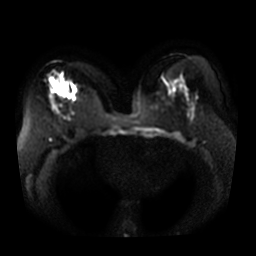
Breast MRI, one axial slice; slice 18 of 36 in the series (ordered by position); diffusion-weighted series; image 2 of 4 stored at this slice position (different b-values; order by instance number); 3 T; 5 mm slice thickness; 256 × 256 image matrix. Female patient.
Outlined on this slice (outlined manually by an expert reader):
- tumour on diffusion-weighted imaging: bounding box [x1, y1, x2, y2] px = [61, 83, 72, 96]